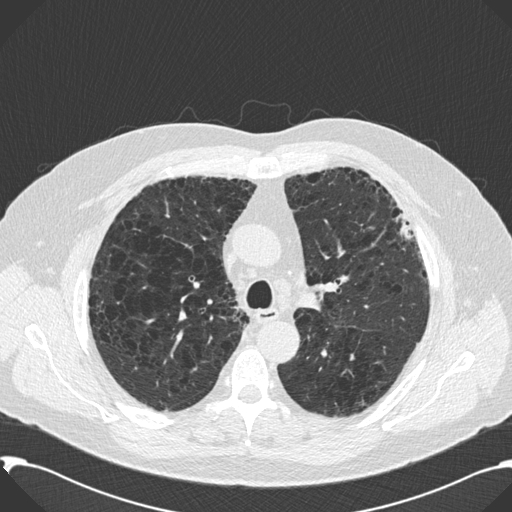
Chest CT (low-dose screening protocol), one axial image. Second annual screen. Lung window (W 1500 / L -600 HU). 120 kVp. Male, age 59 years at enrolment.
Expert reader's lesion annotation, bounding box <360,189,428,291> (left, top, right, bottom; pixels). Screening reader's record for this exam: no non-calcified nodule ≥4 mm recorded. Official screen result: negative screen, significant abnormalities not suspicious for lung cancer.